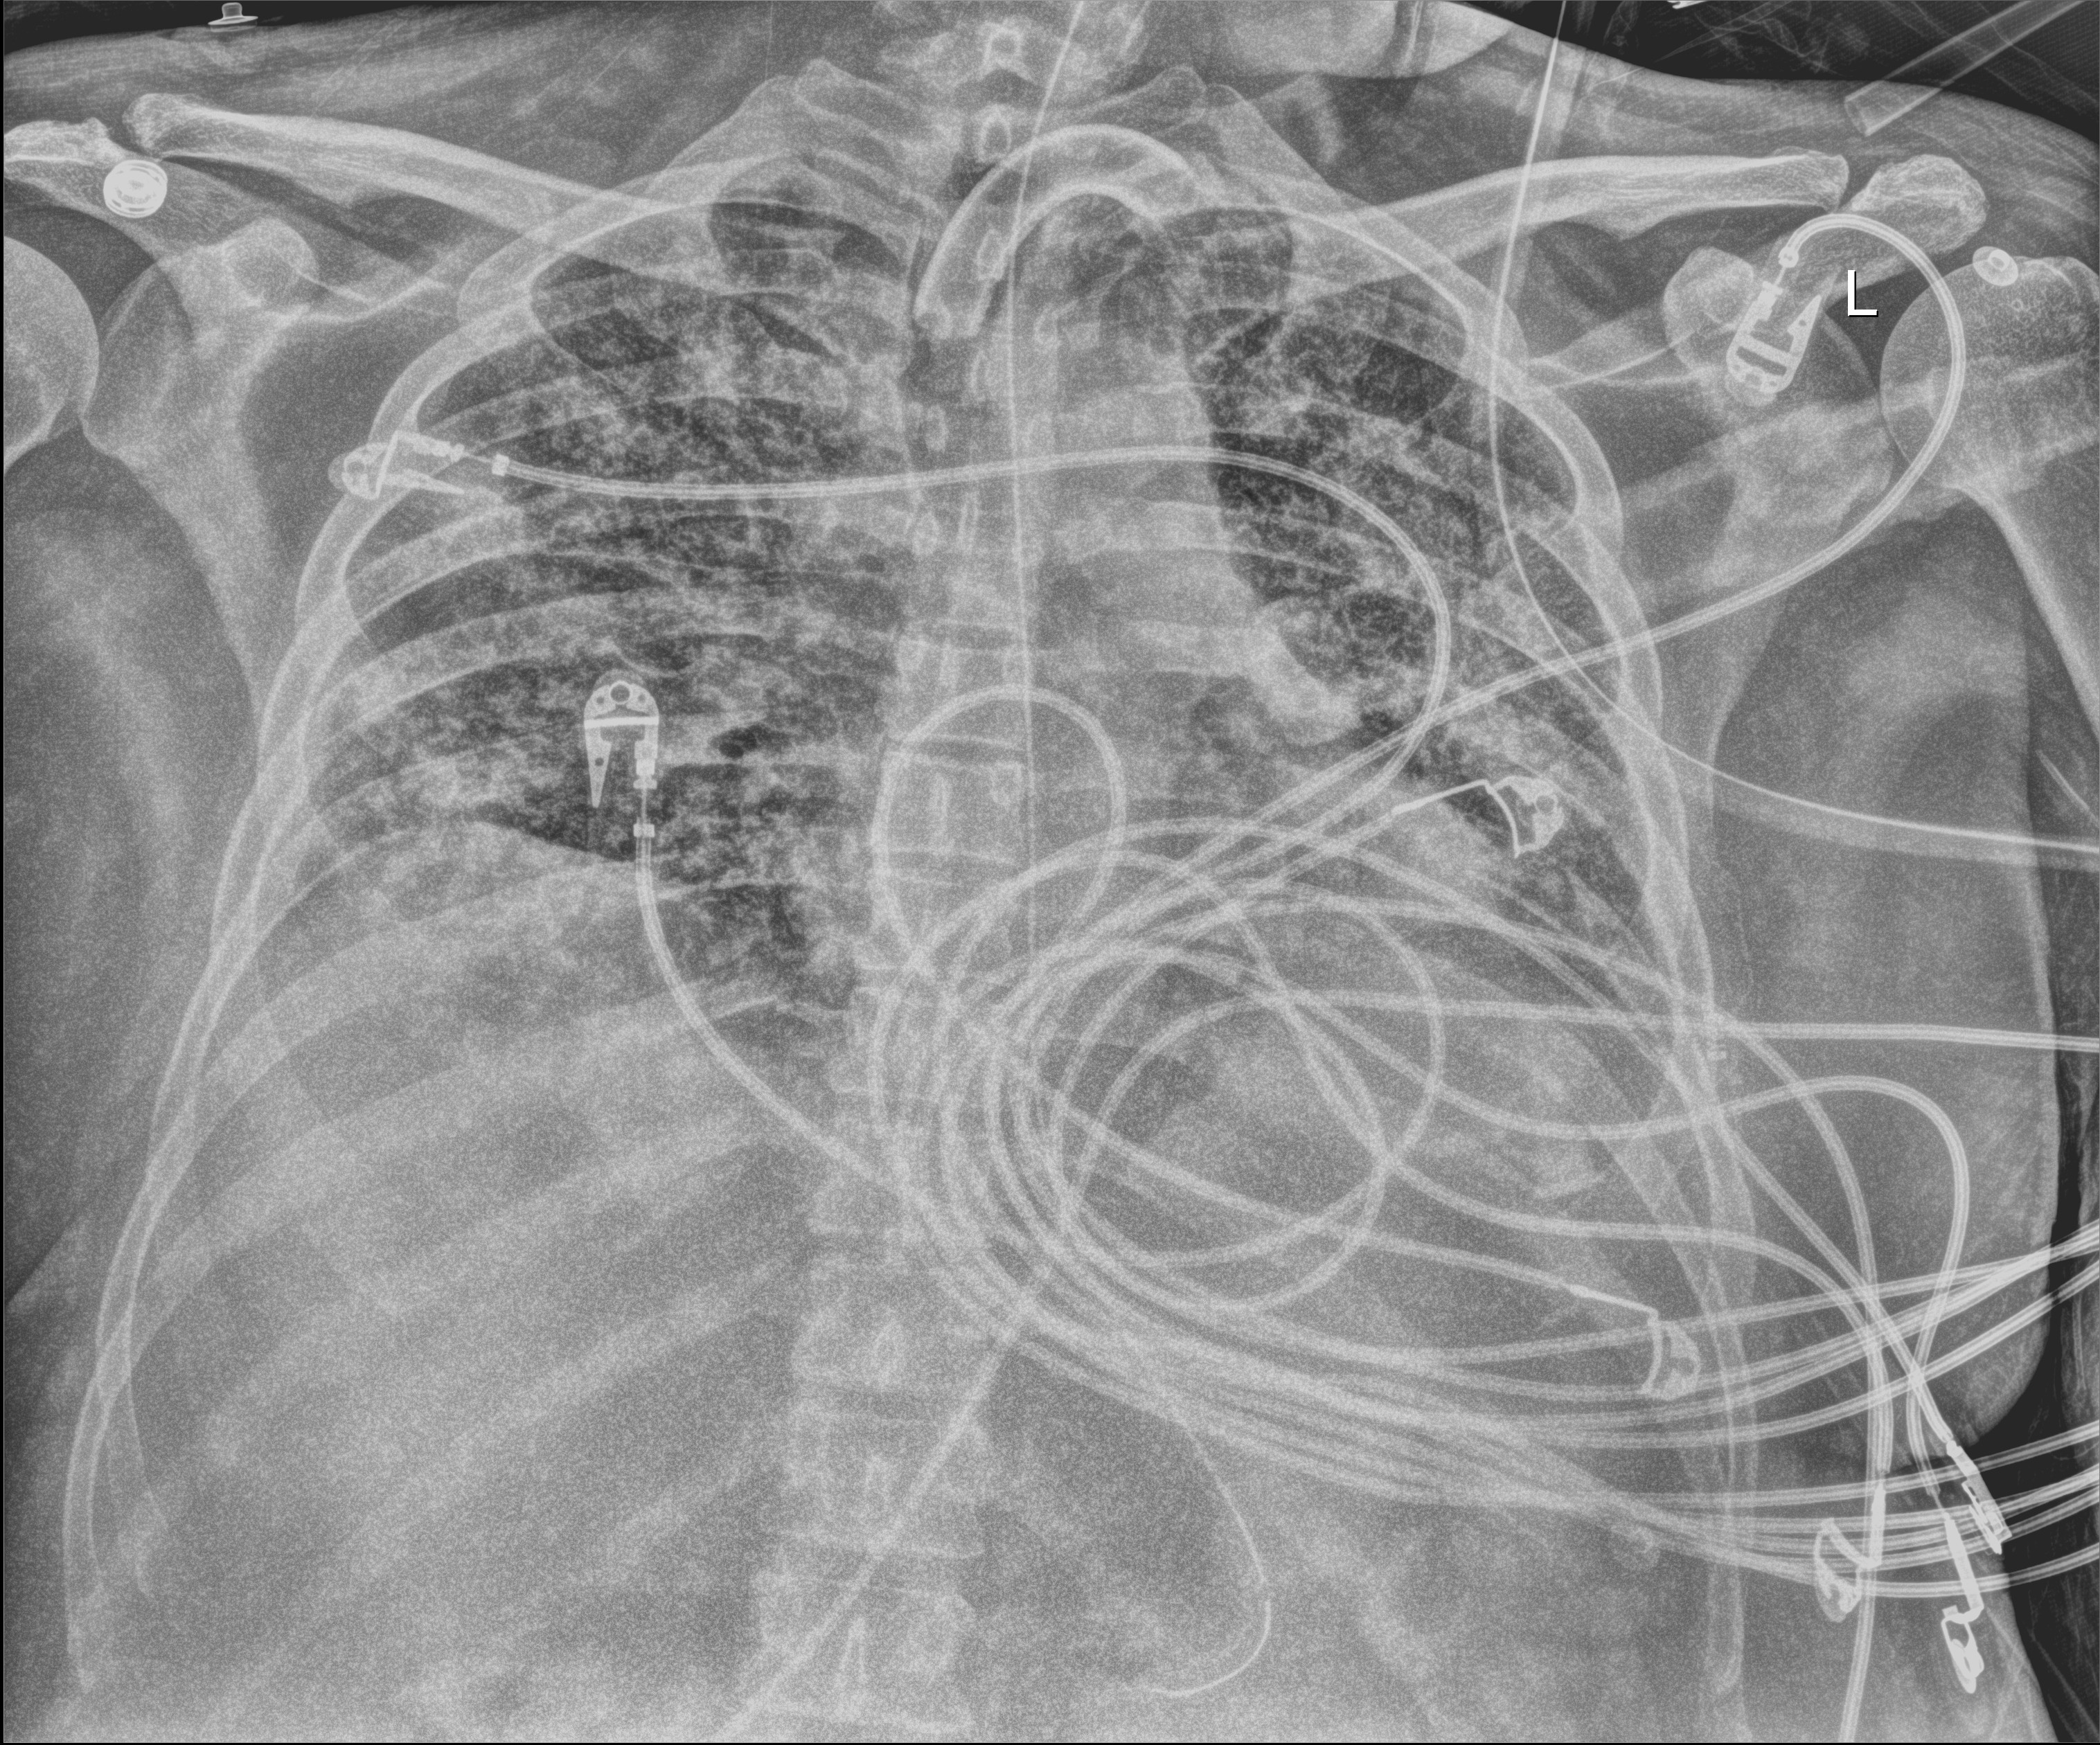
Bedside chest radiograph (digital radiography); anteroposterior (AP) projection. Patient hospitalised with COVID-19; male, aged 18–59 years.
Hospital-stay facts (about this admission, not read from this image; timing relative to this image not recorded): mechanically ventilated during this hospital stay: yes.